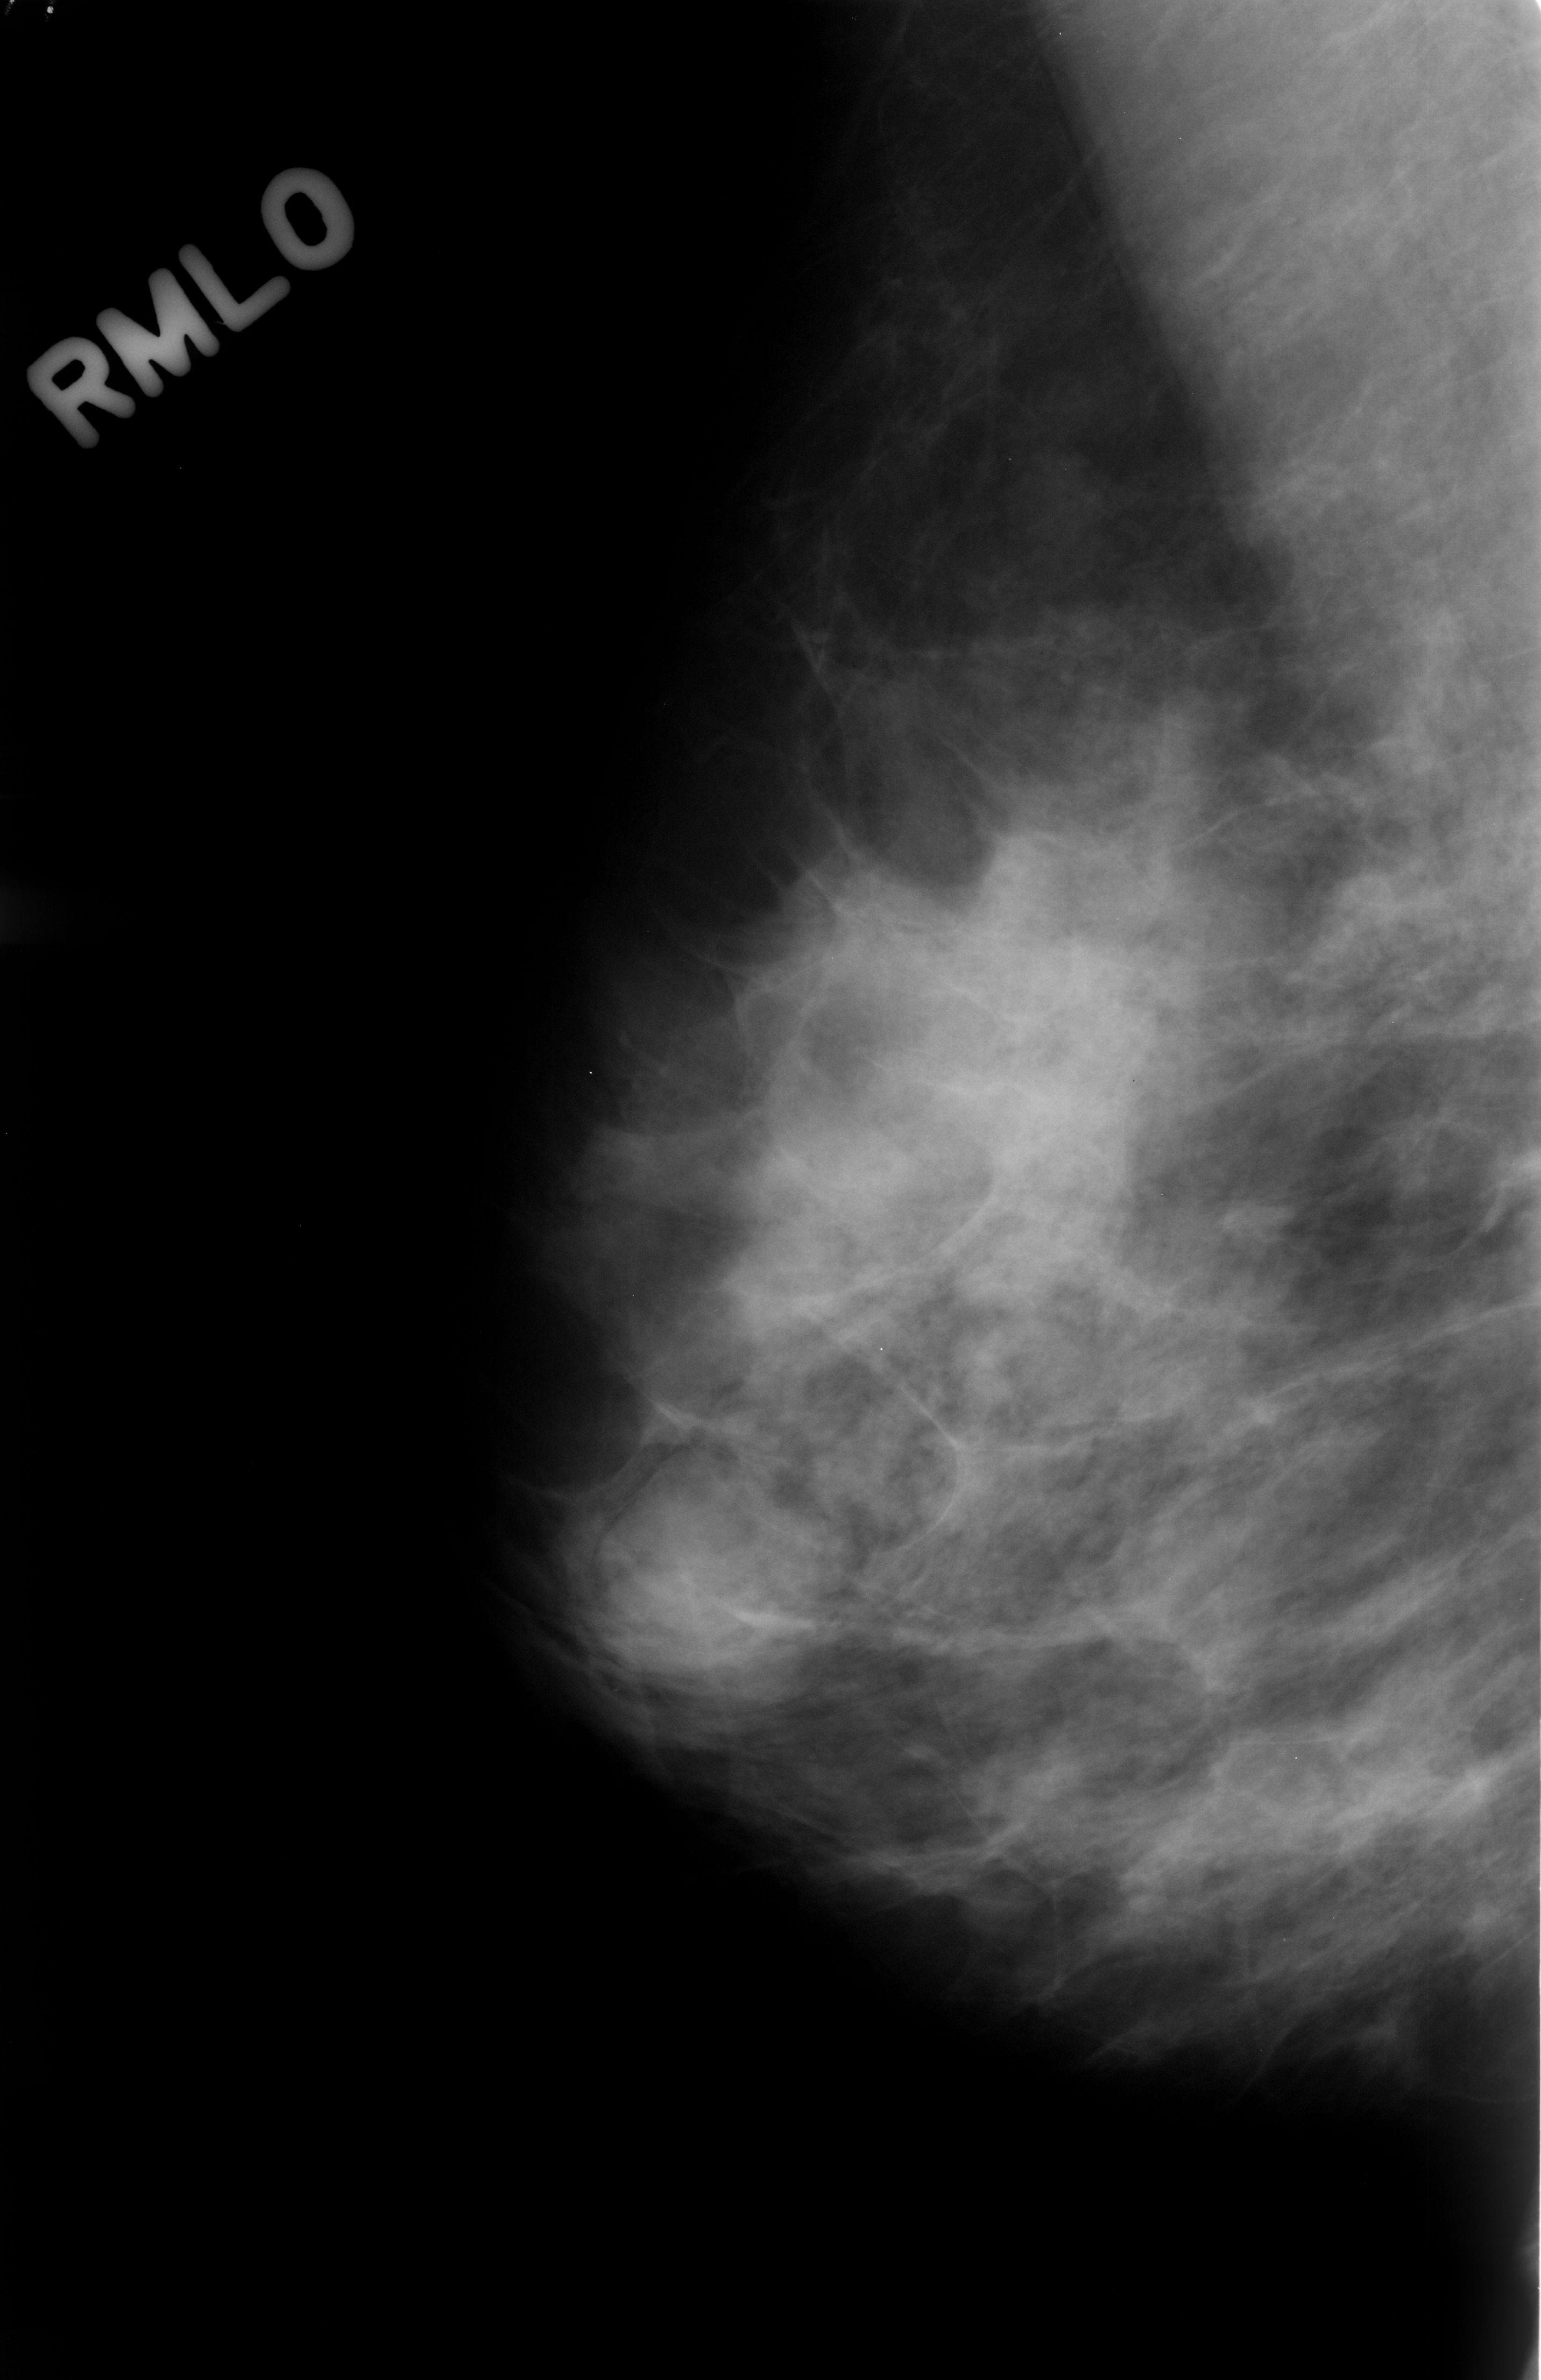
Scanned film-screen mammogram, right breast, mediolateral oblique (MLO) view, breast composition: scattered fibroglandular densities (BI-RADS density category 2 of 4).
Mass, shape lobulated, margins circumscribed; BI-RADS assessment category 4; pathology result (as recorded, not read from the image): benign.